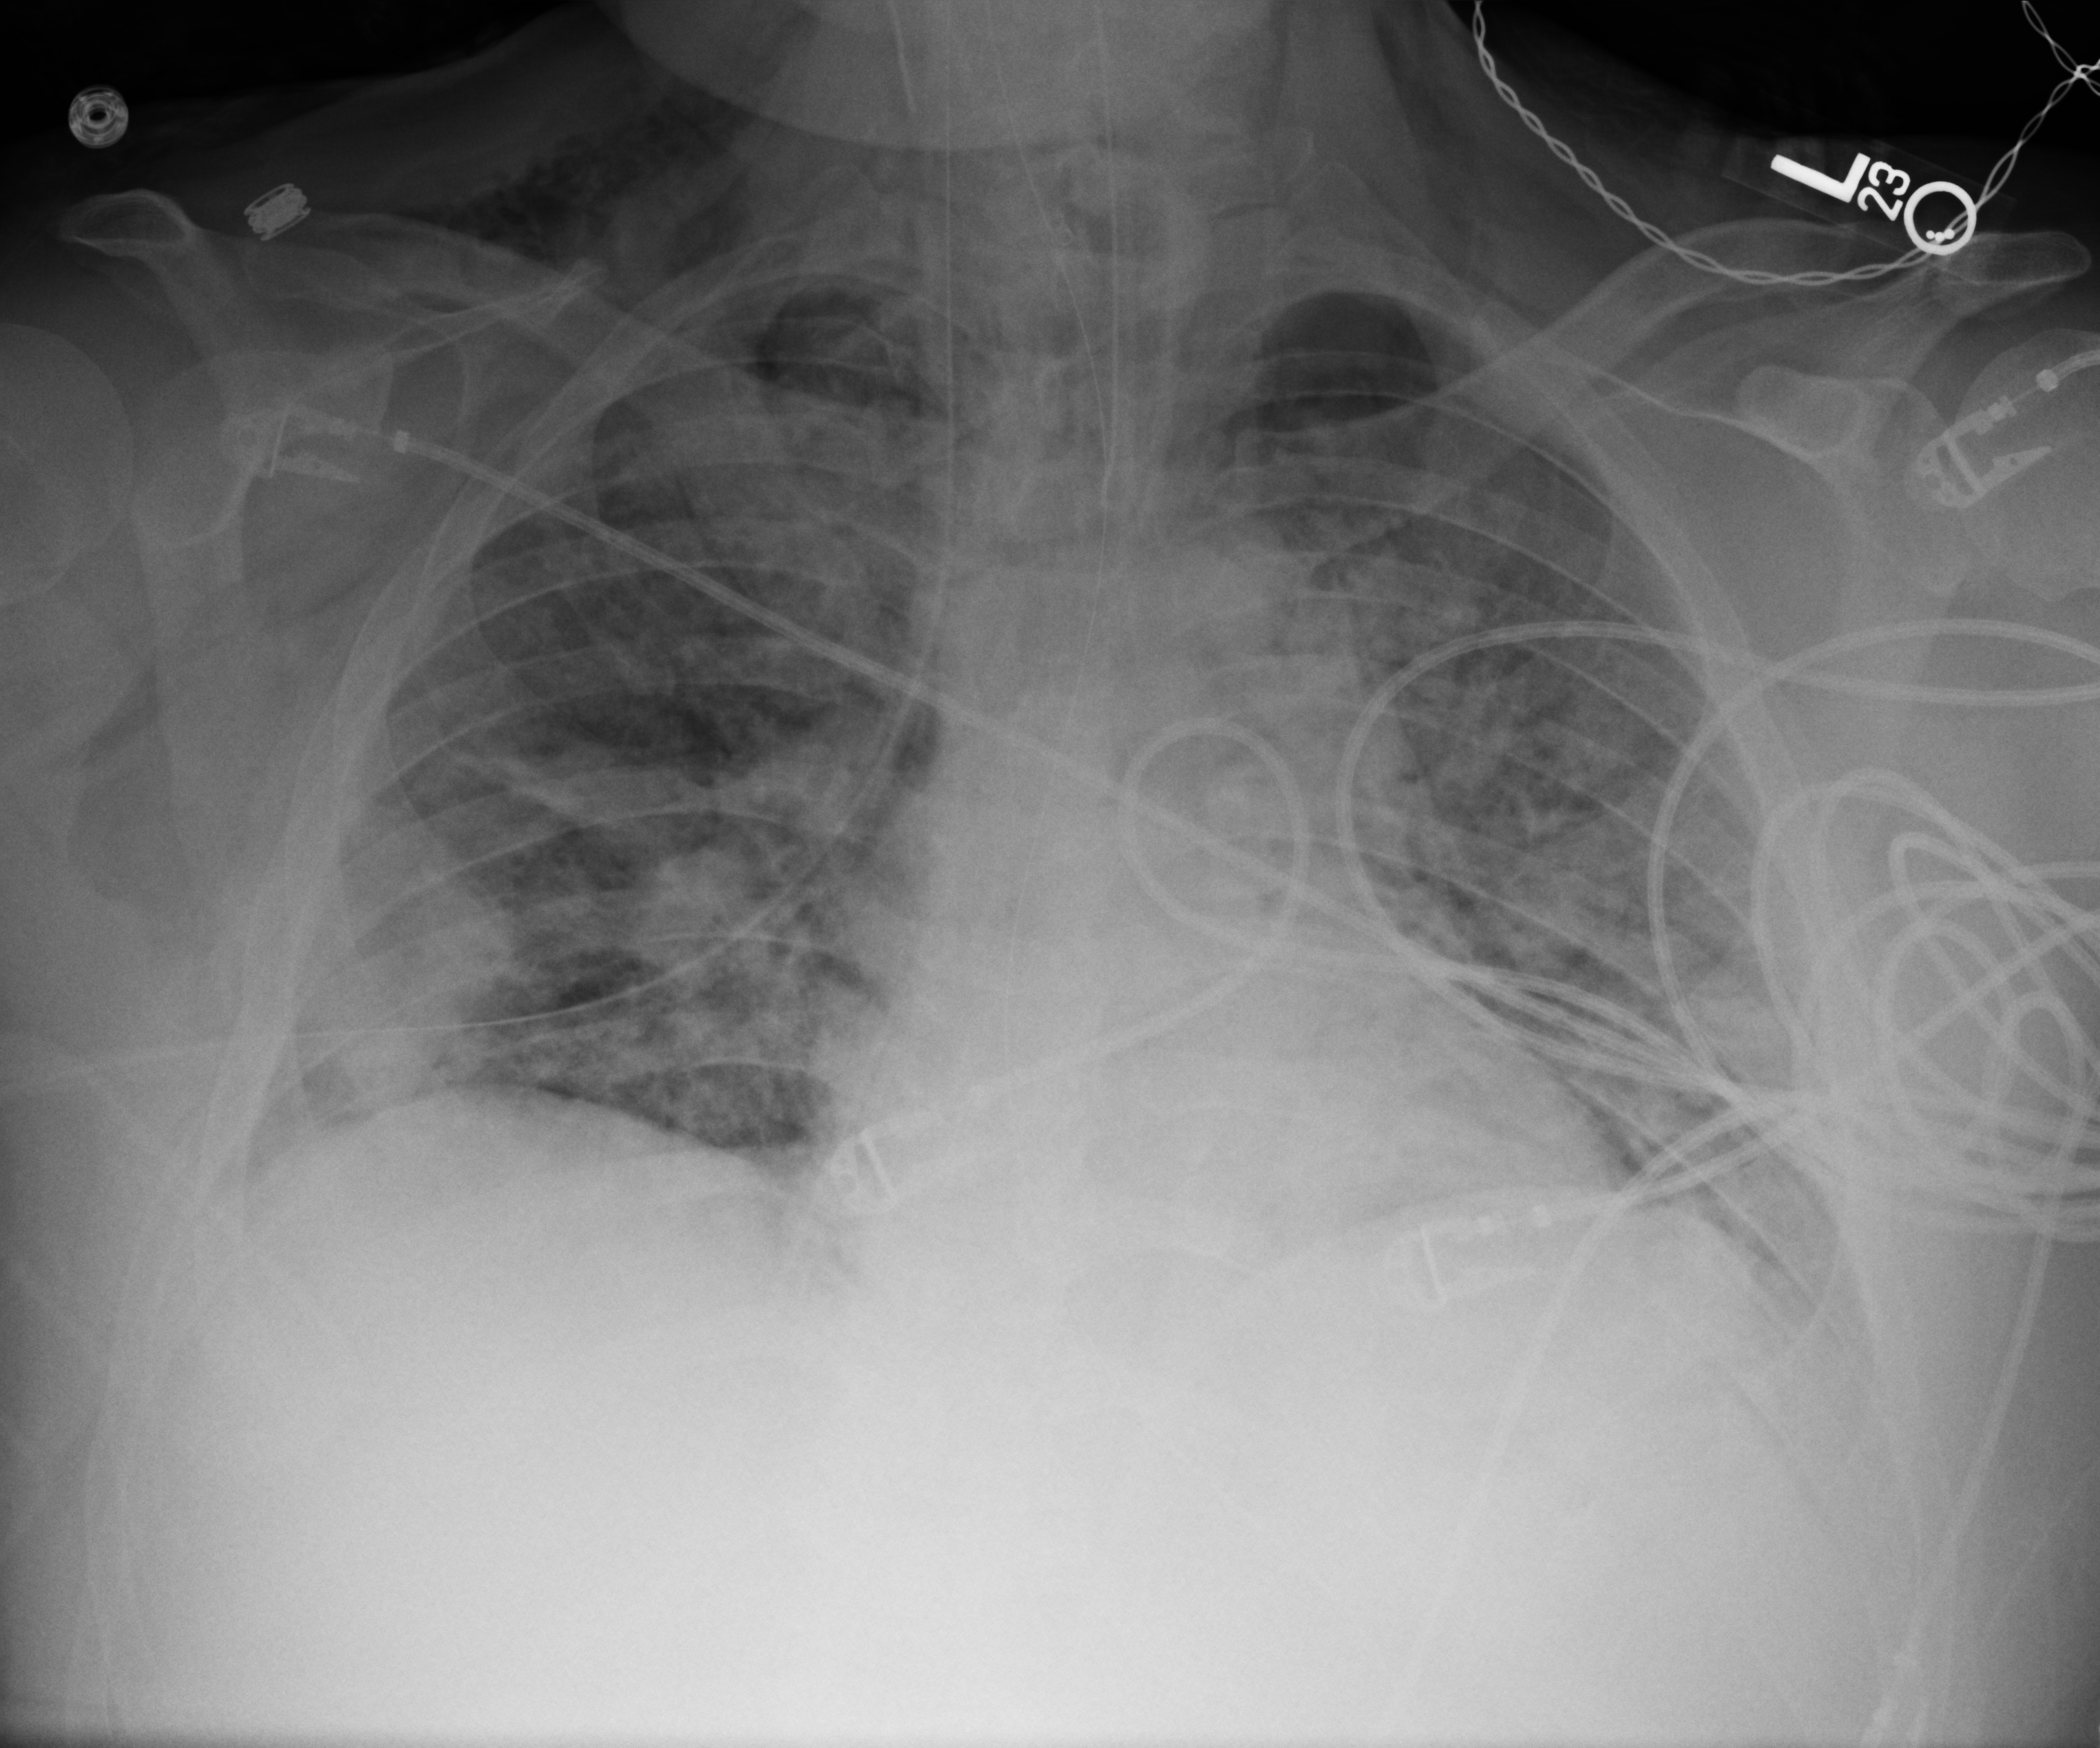
Portable chest radiograph. Adult patient hospitalised with COVID-19, age 18–59 years.
Hospital-stay facts (about this admission, not read from this image; timing relative to this image not recorded):
- admitted to intensive care during this hospital stay: yes